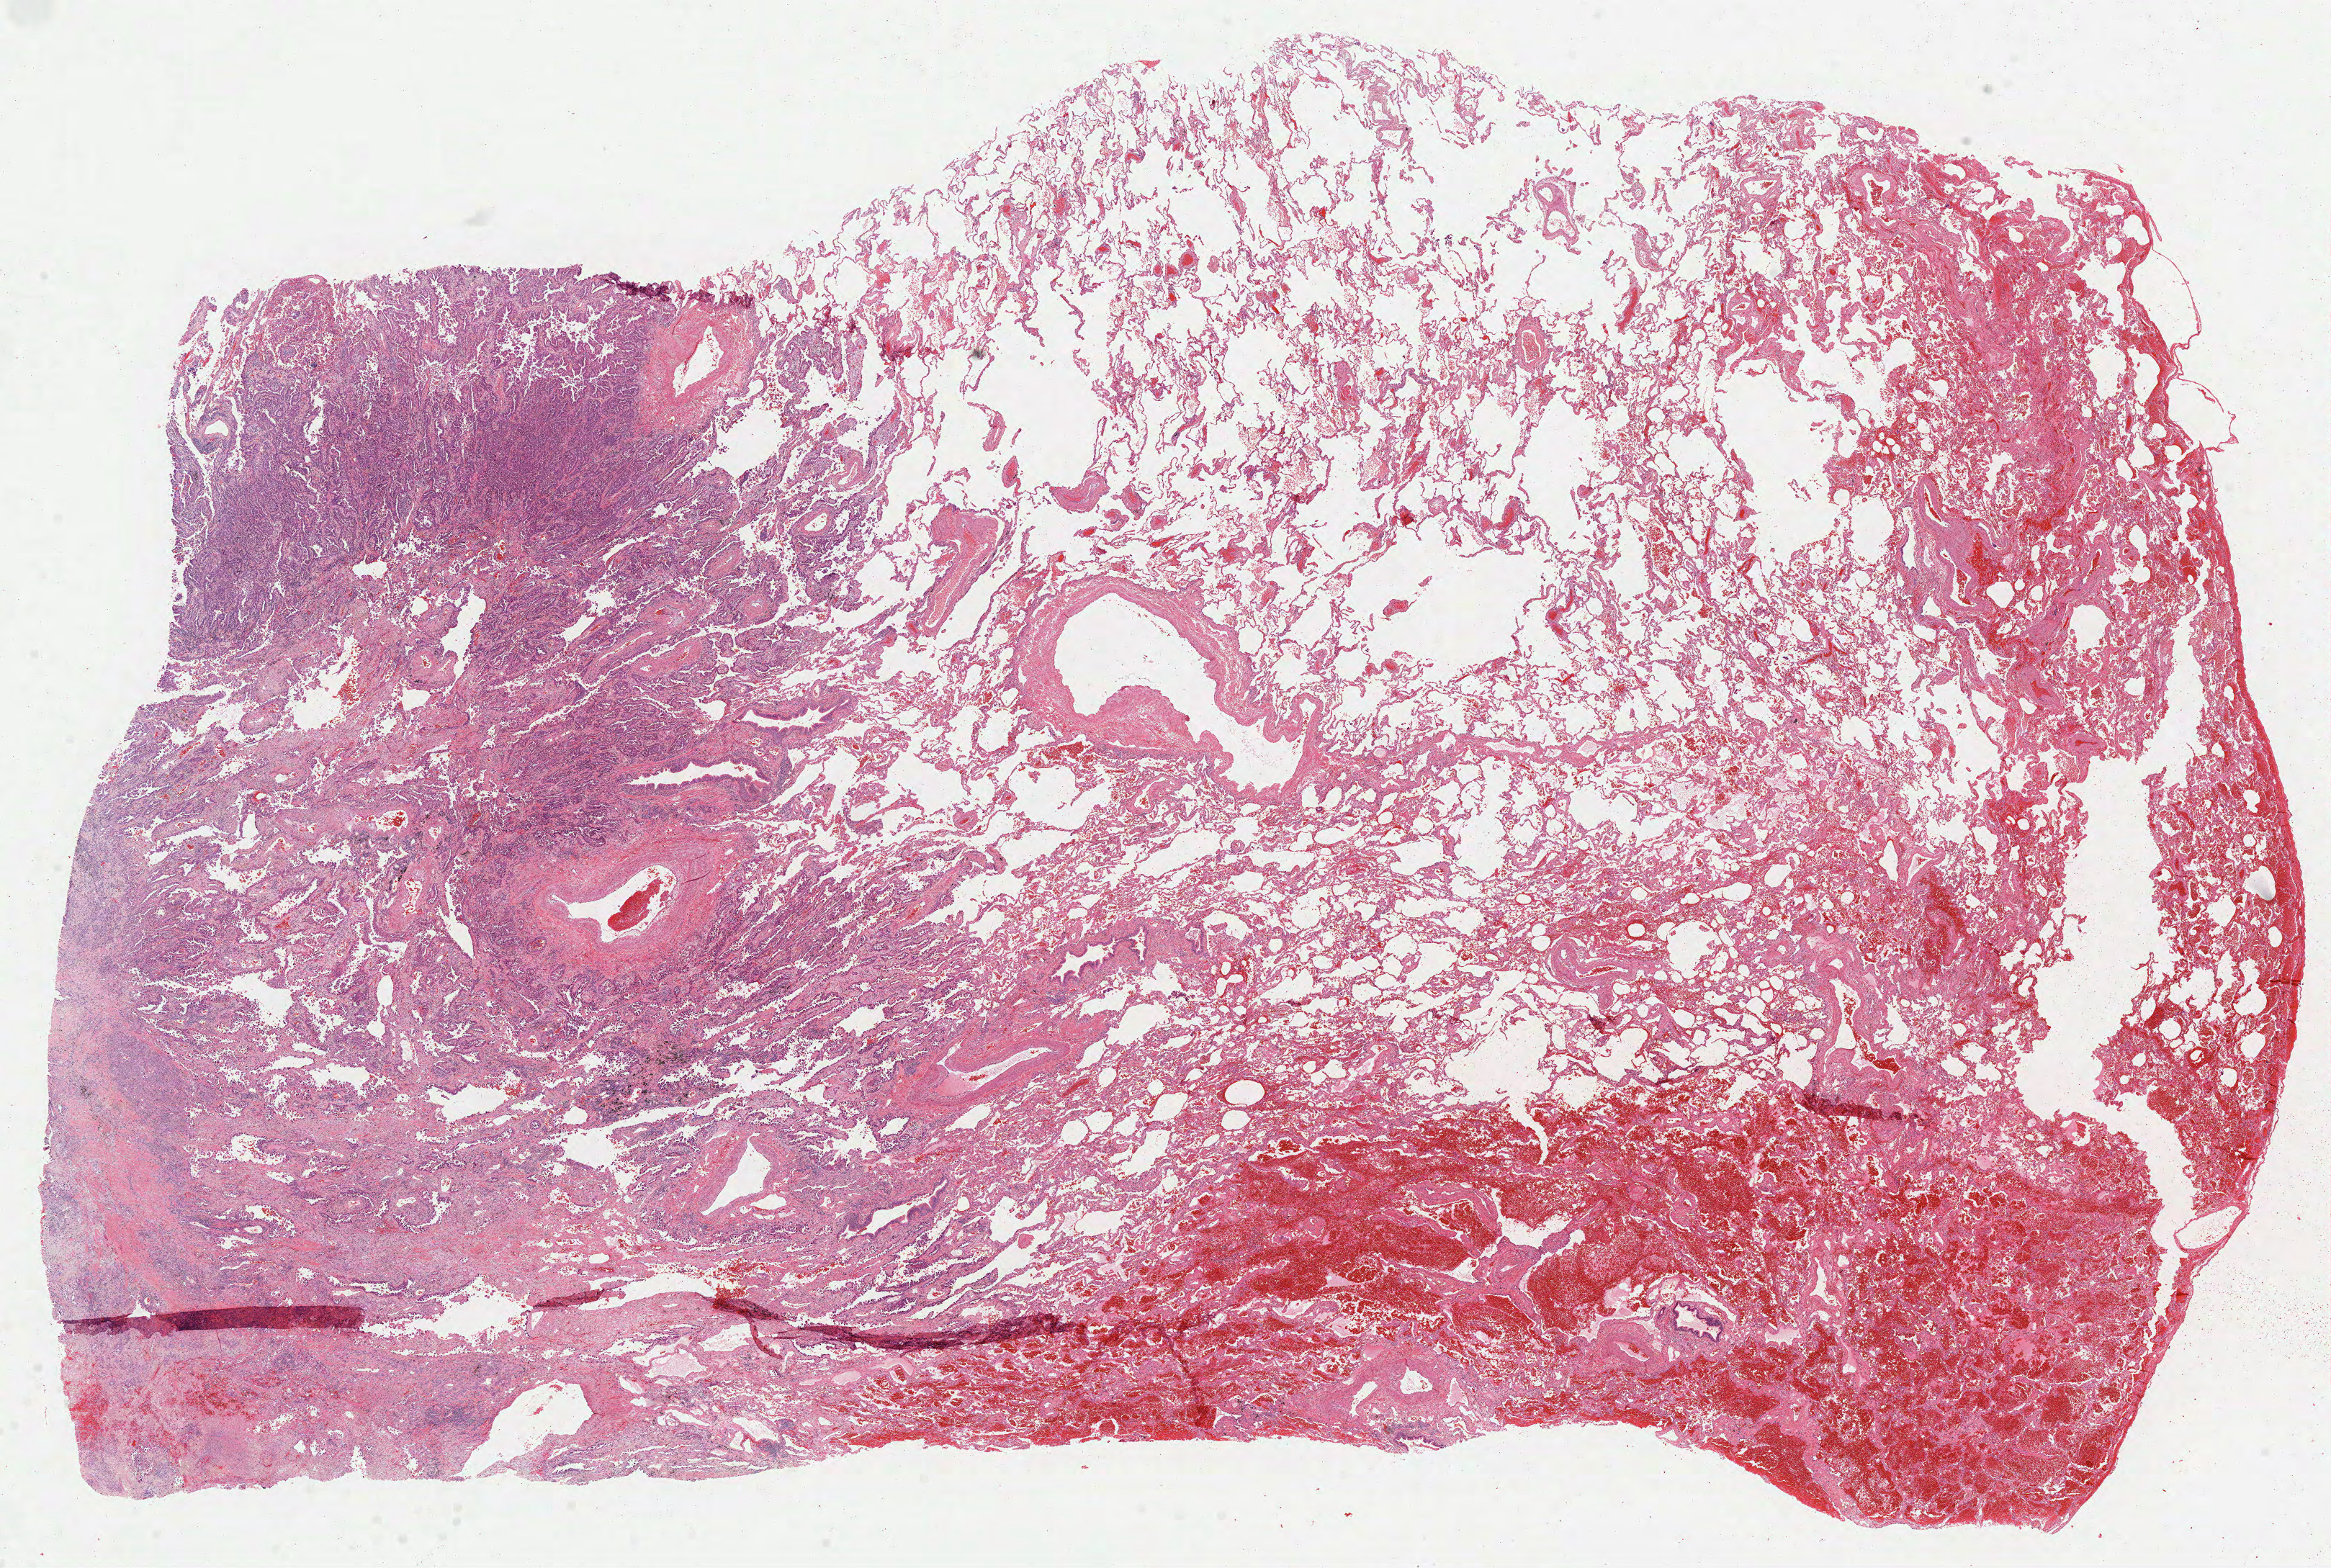
Digitized H&E tissue section (whole slide), shown as a low-resolution overview of the whole scanned area (about 26.1 x 17.6 mm, slide scanned at 40x). FFPE section. Lung, primary tumour sample. Female patient; age at initial diagnosis 66 years.
Diagnosis: Invasive micropapillary carcinoma. AJCC pathologic stage: IIB.